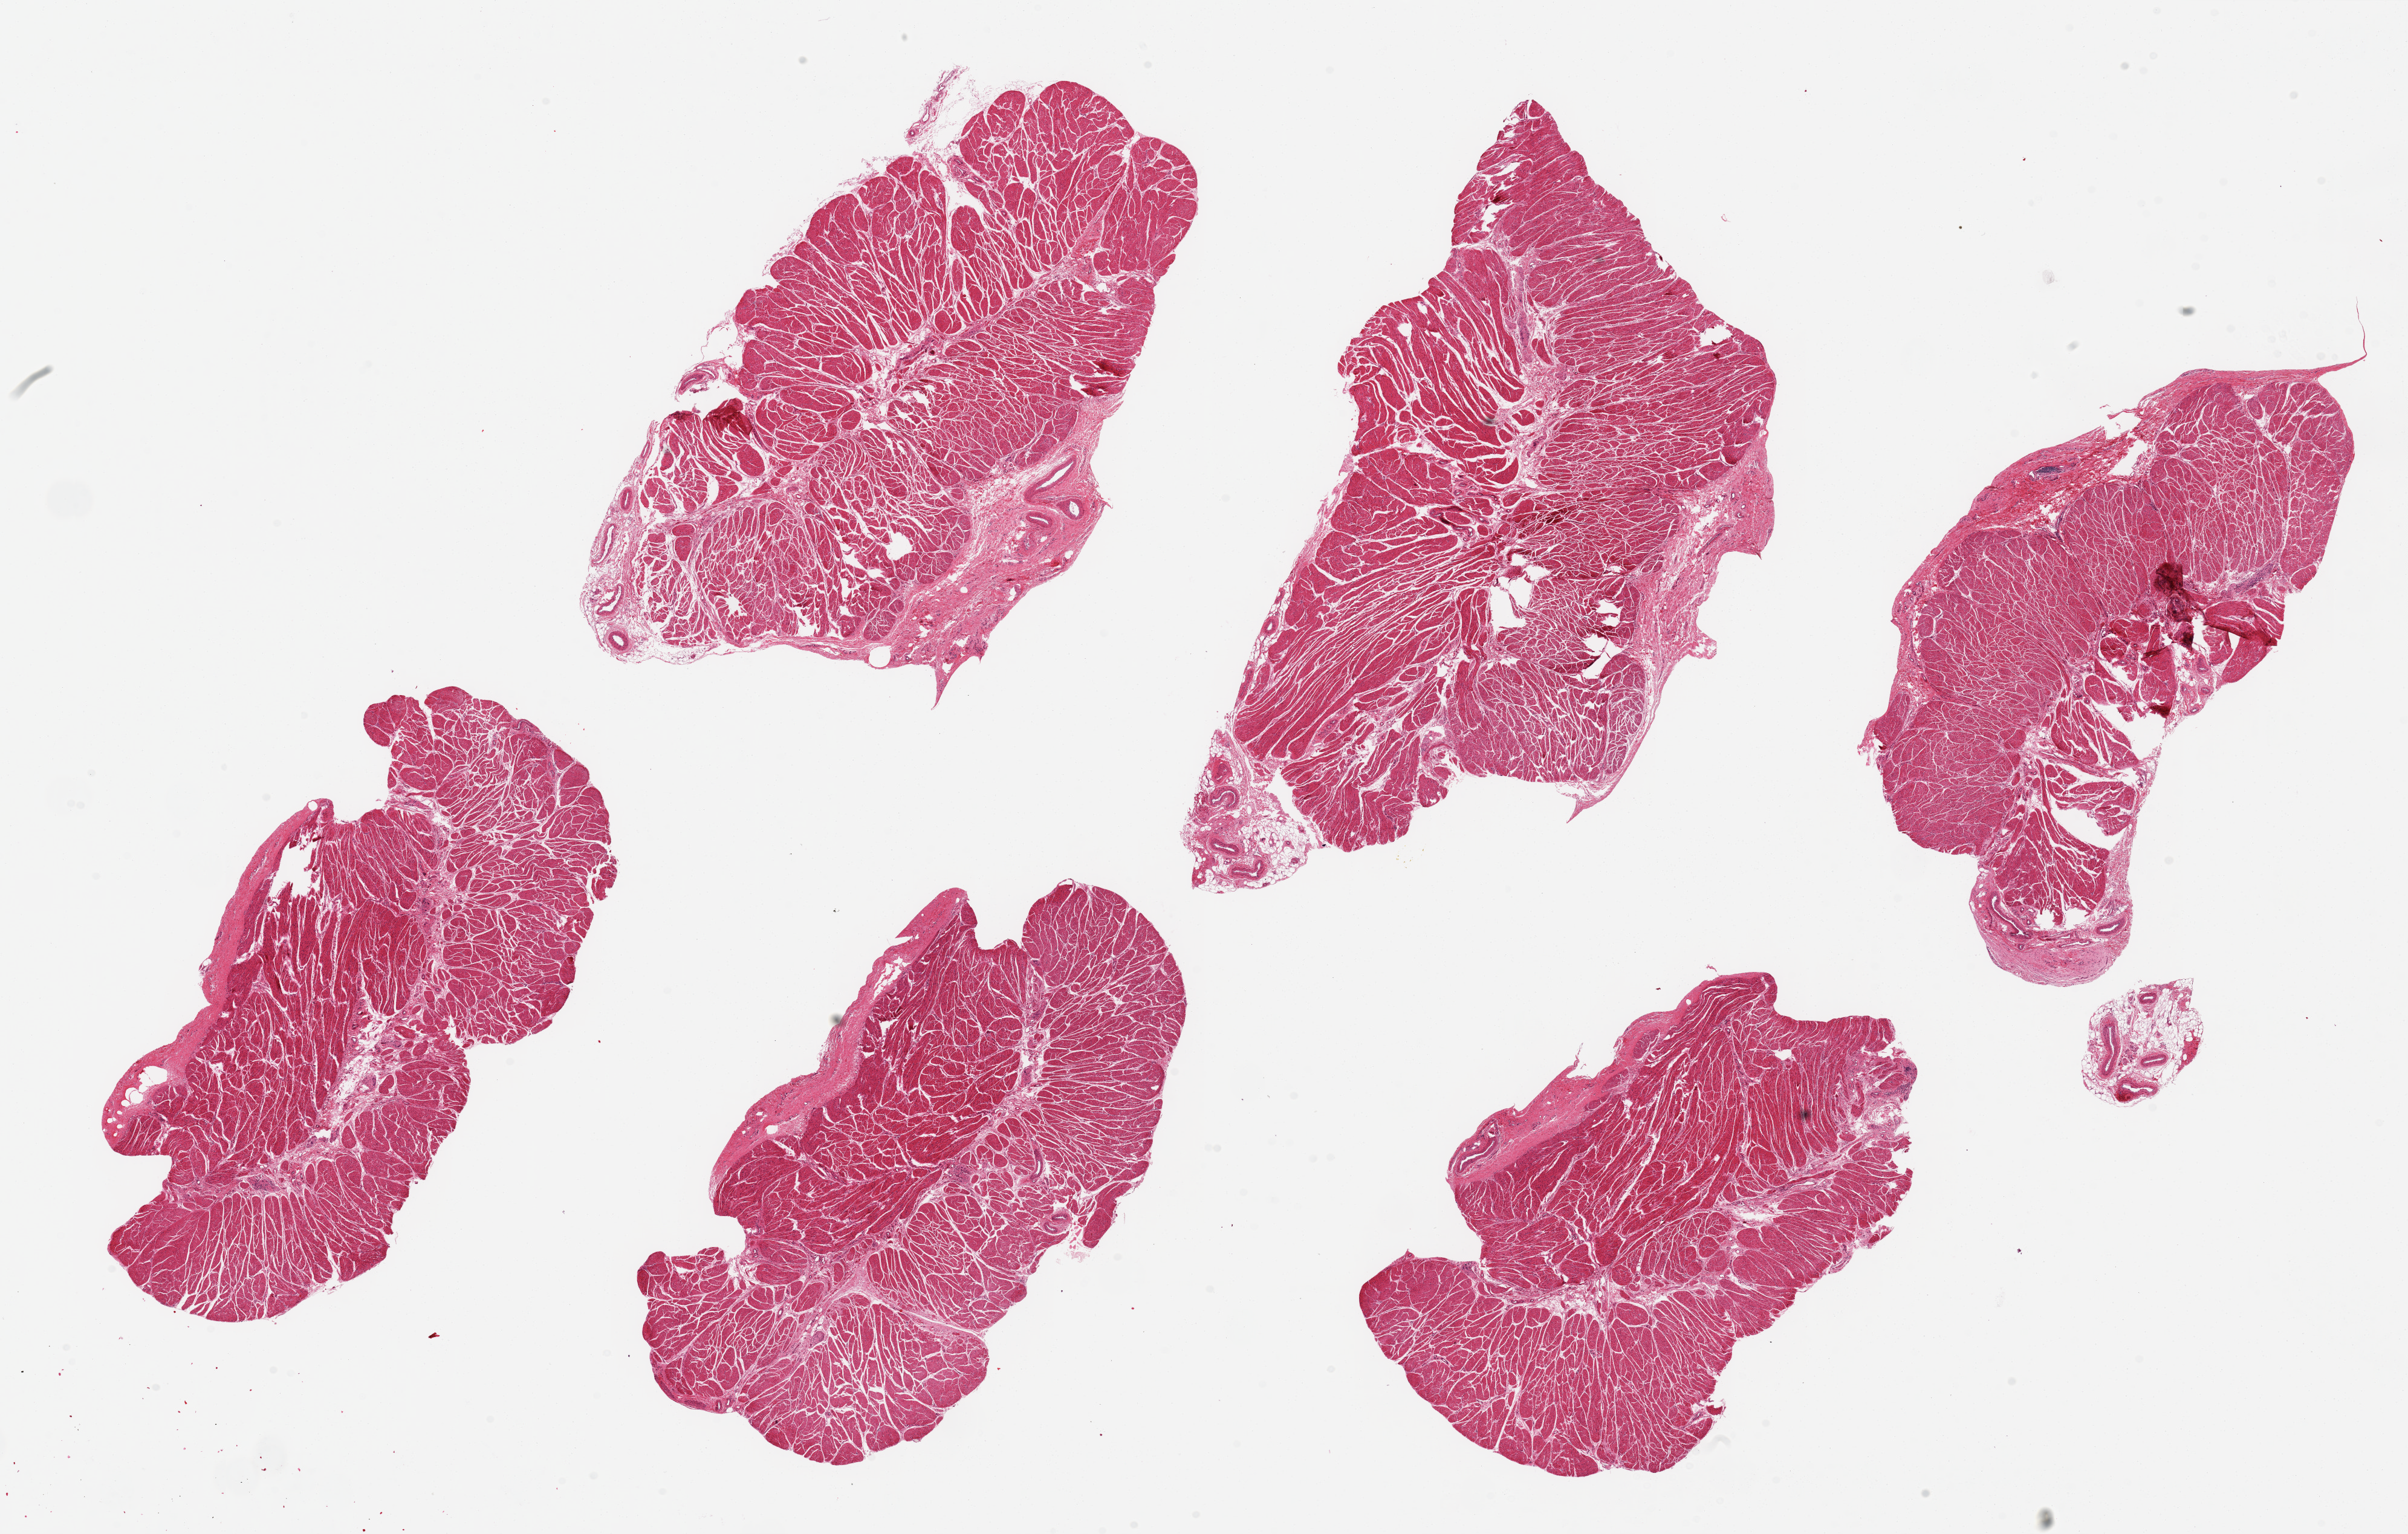
Haematoxylin and eosin whole-slide image, whole scanned area (about 31.5 x 20.1 mm) shown as a low-resolution overview. PAXgene-fixed paraffin-embedded (PFPE) section. Section of esophageal muscle (target tissue). Donor tissue sample. Donor: male.
* pathologist's review note for this sample: 6 pieces up to 10x5.6 mm